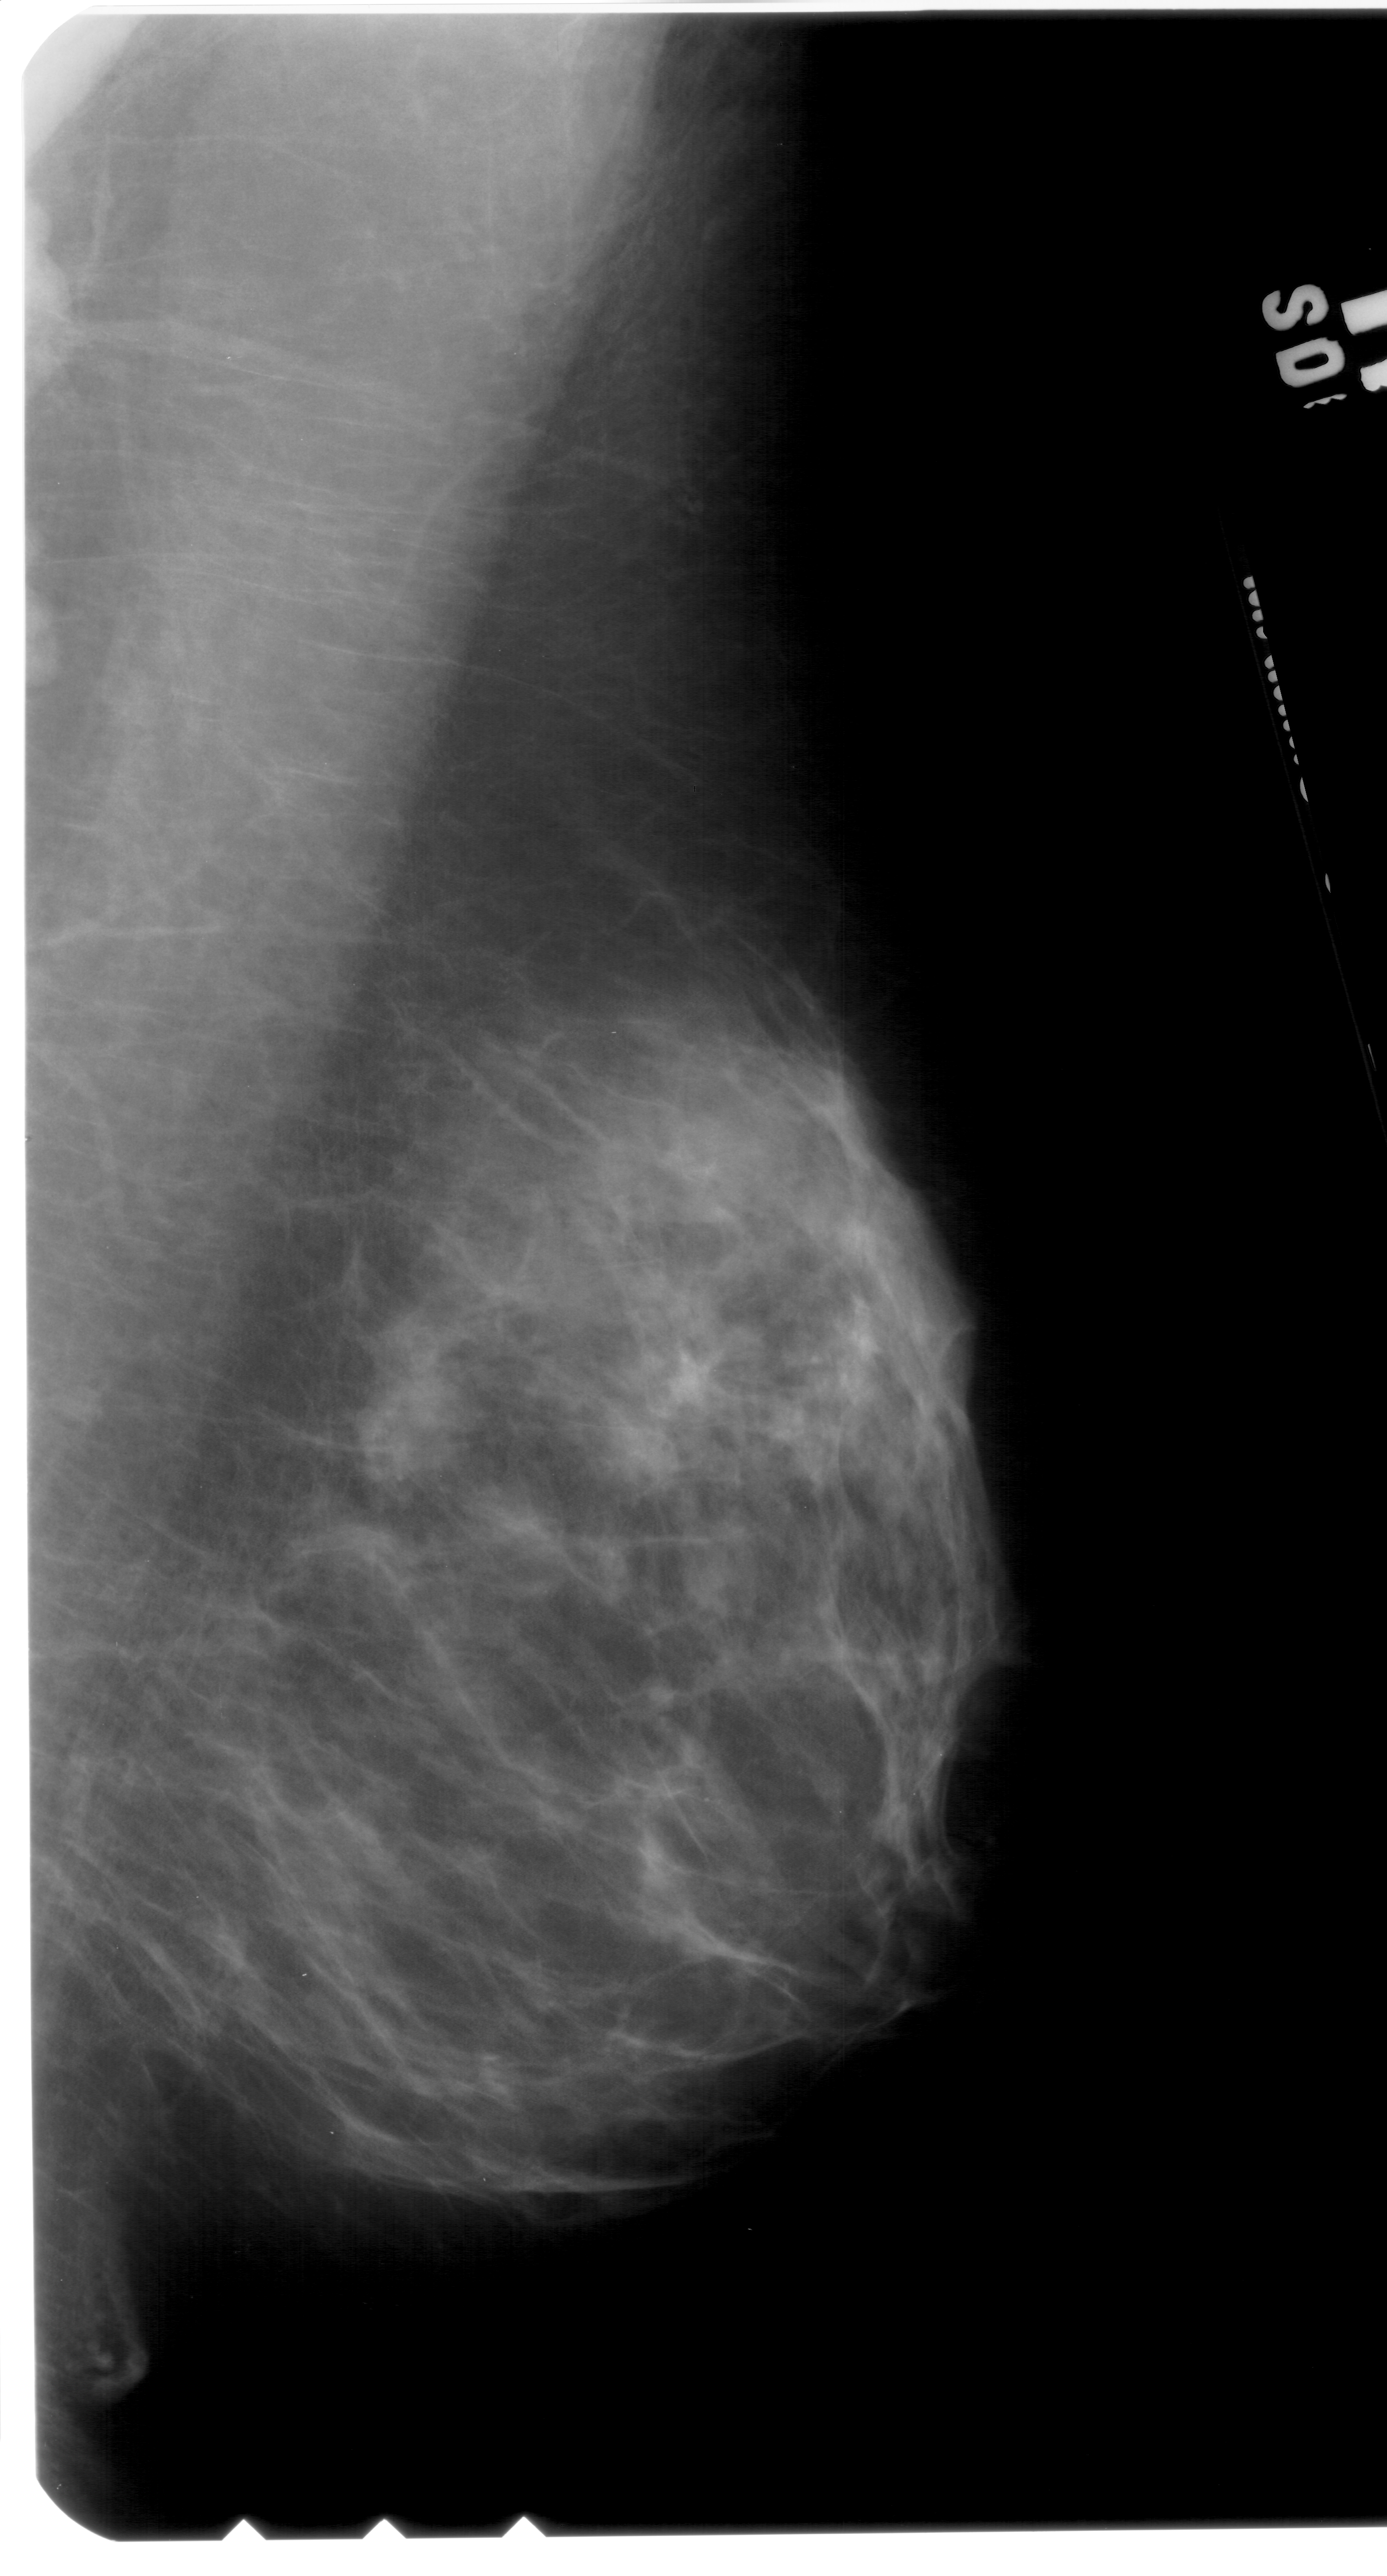
Digitized screen-film mammogram; right breast; mediolateral oblique (MLO) view.
Abnormality record for this image: calcifications, morphology pleomorphic, distribution clustered; BI-RADS assessment category 4; subtlety rating 1 on a 1 (subtle) to 5 (obvious) scale; pathology (as recorded): benign.